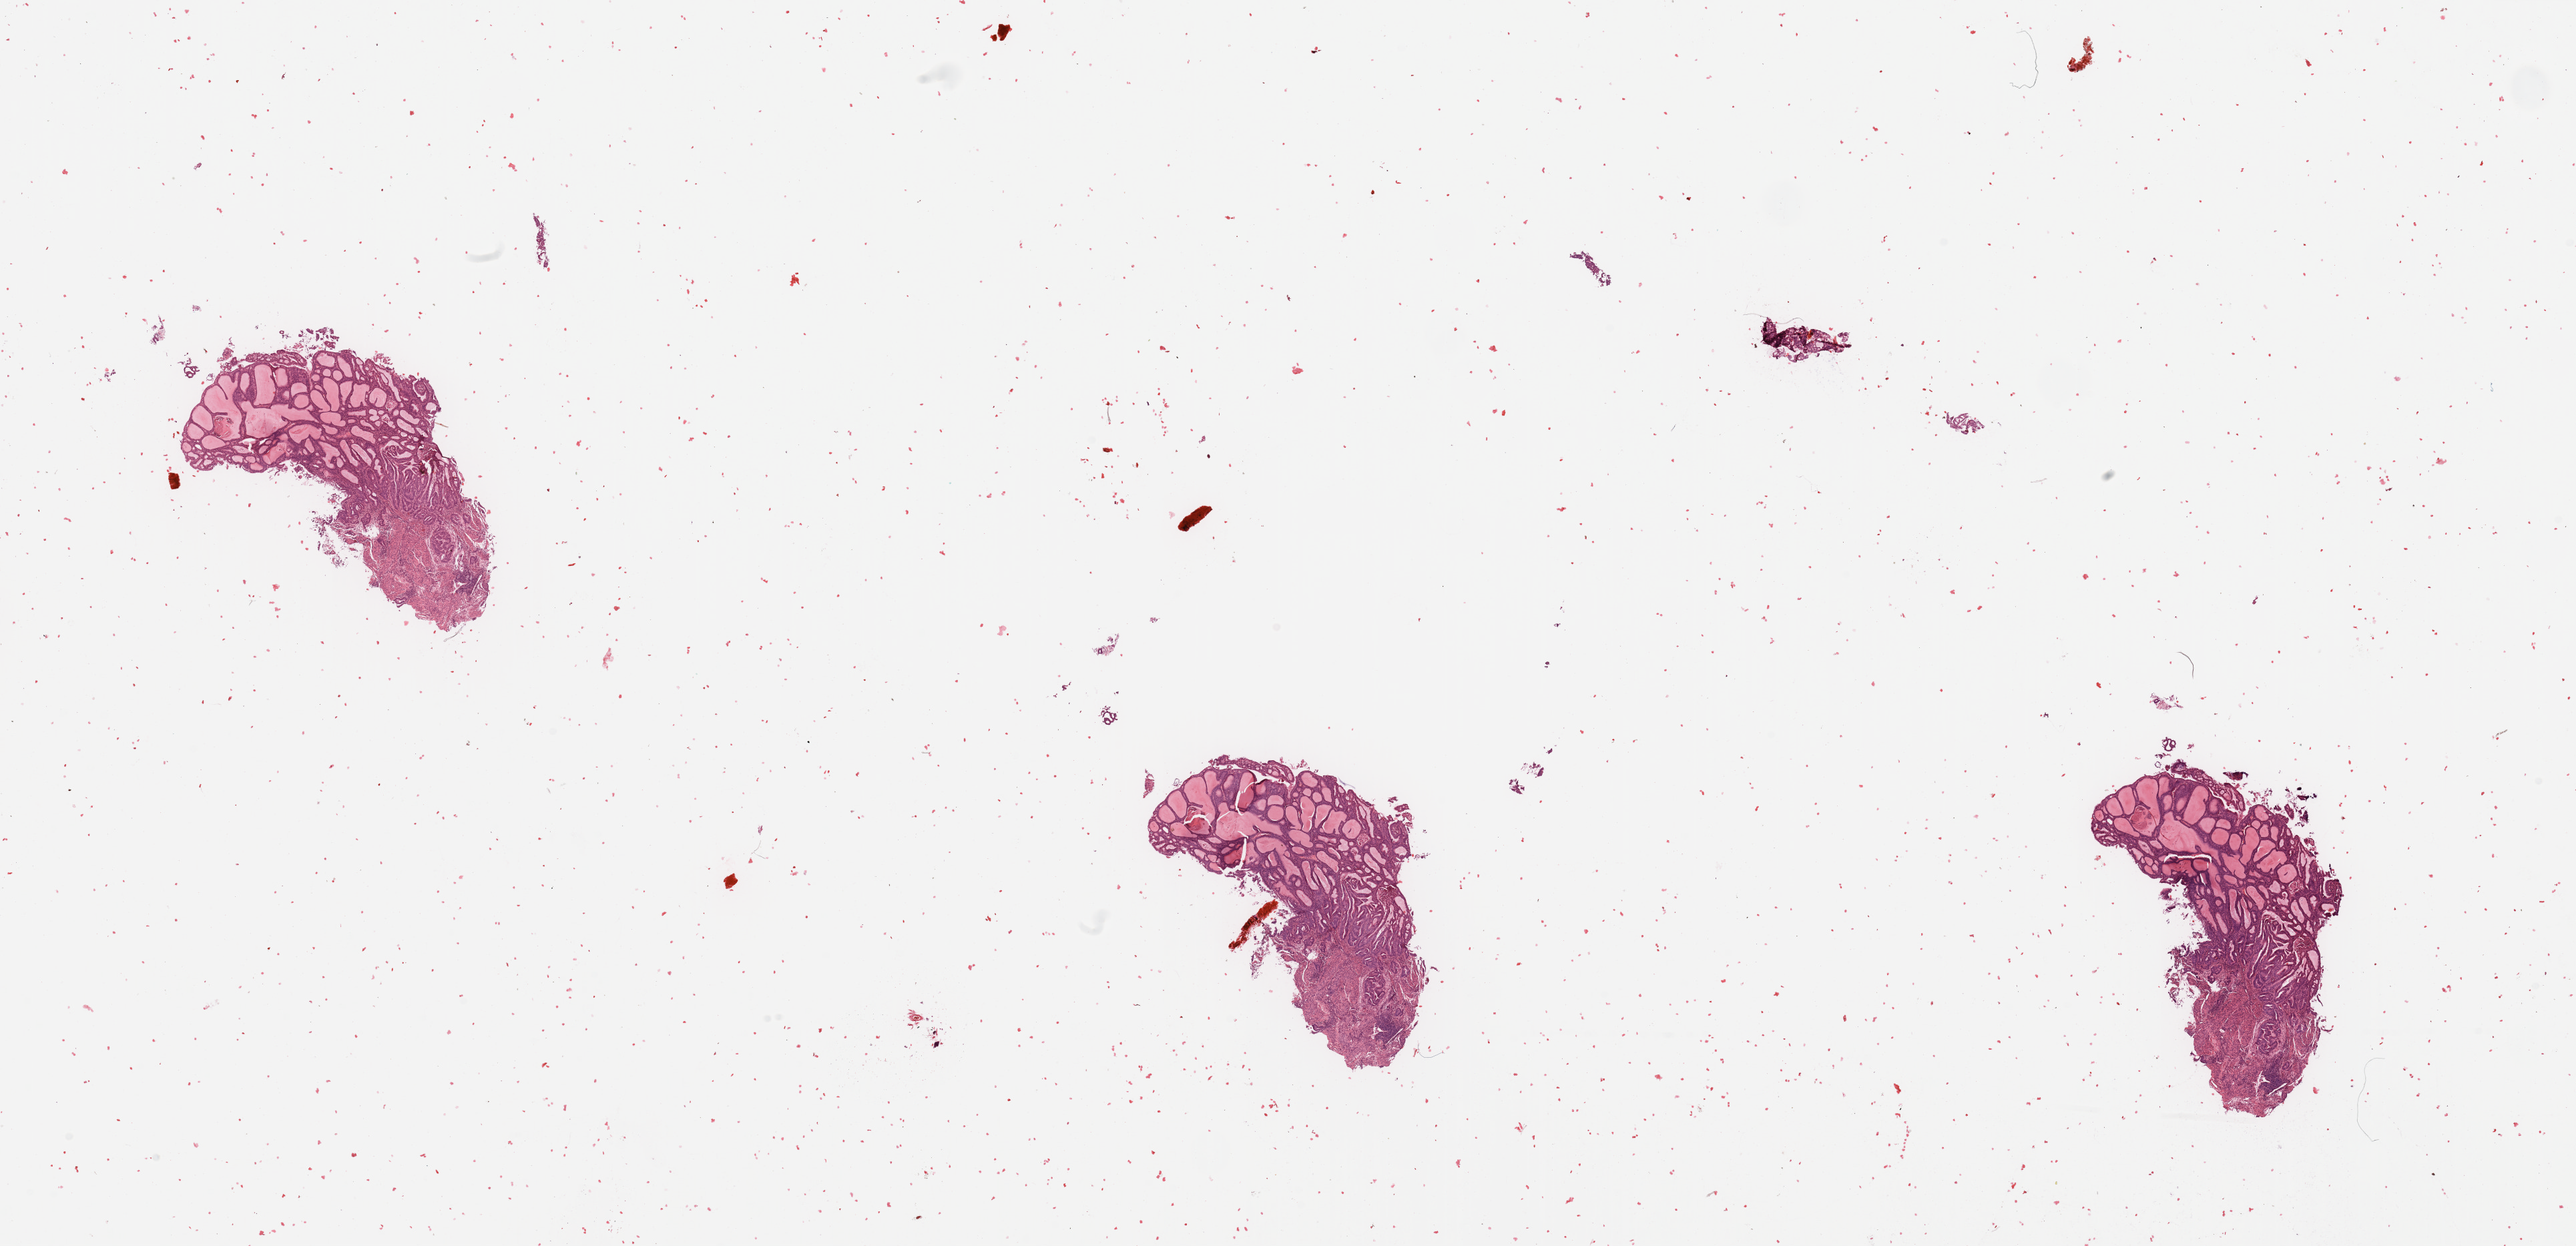
Hematoxylin and eosin (H&E) stained whole-slide image — shown as a low-resolution overview of the whole scanned area (about 30.5 x 14.8 mm), tumour tissue sample, sampled site: uterus. Patient: female, age 73 years. Histologic grade: G2 (moderately differentiated). Slide review estimates, as recorded: tumour nuclei 80%, necrosis 2%.
AJCC pathologic stage: III. Primary tumour site (as recorded): anterior endometrium. Histologic diagnosis: Endometrioid adenocarcinoma, NOS.